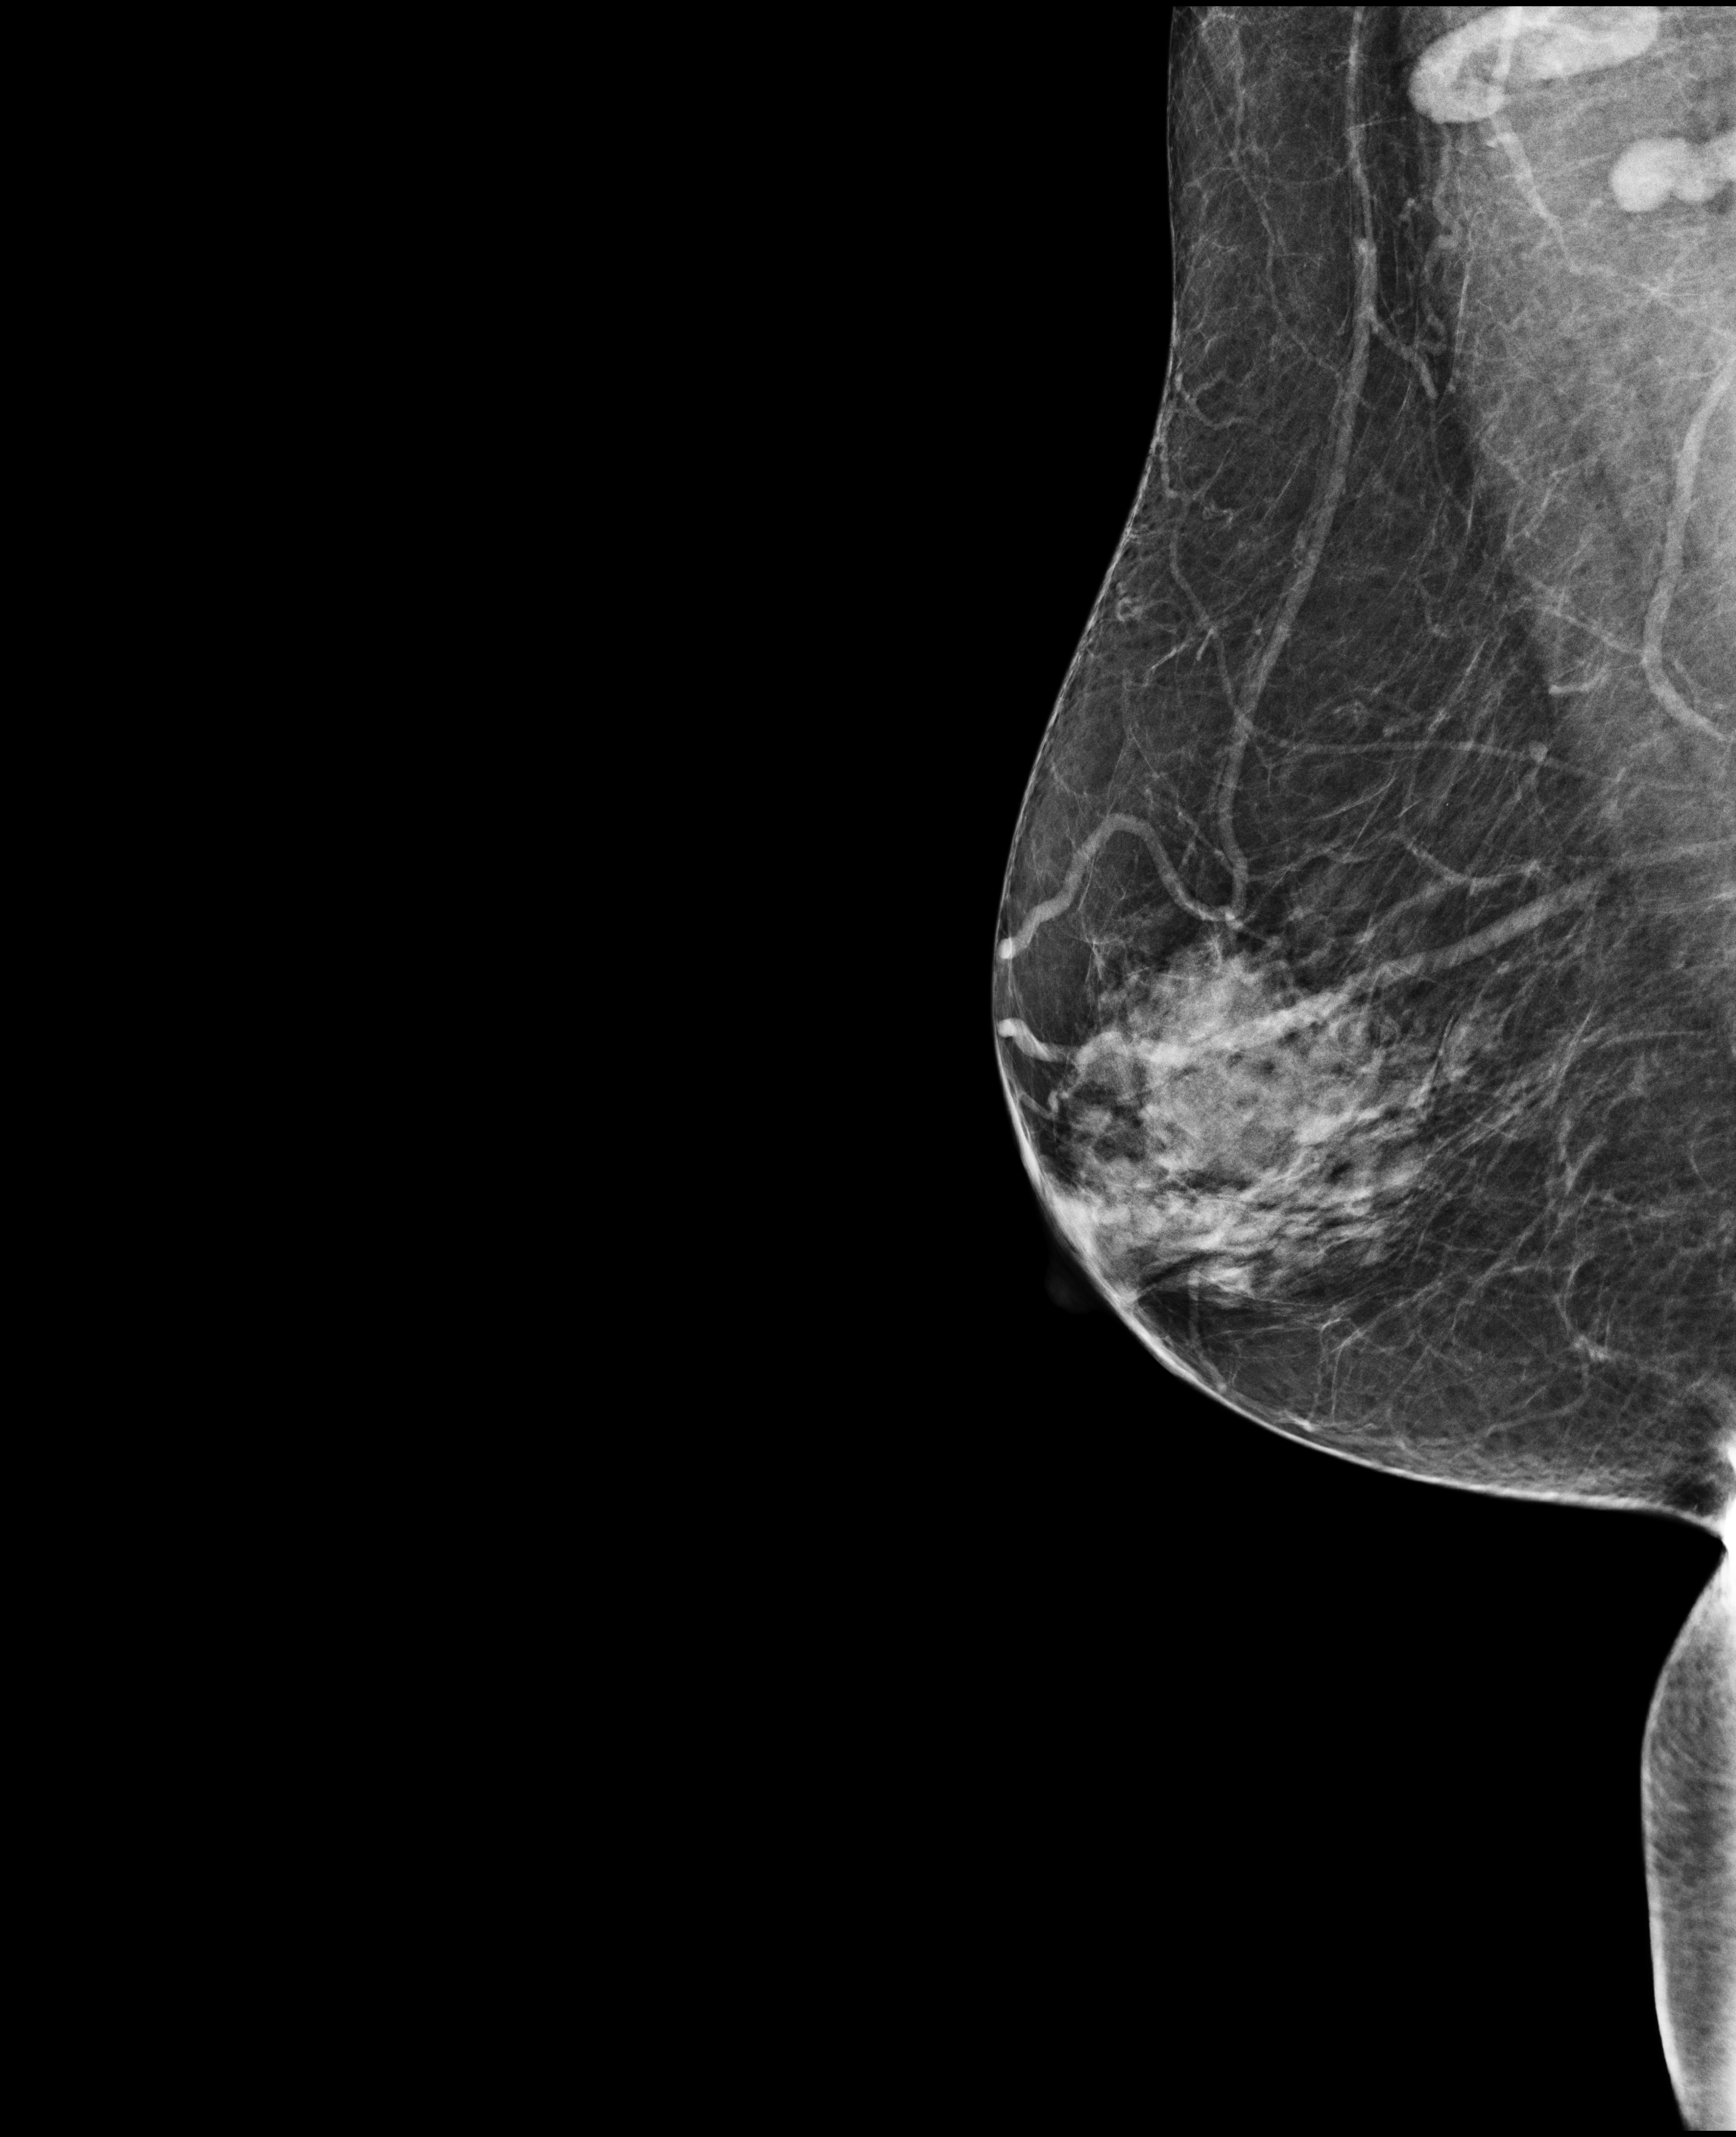
Full-field digital mammogram (FFDM), right breast, MLO view, screening examination, compressed breast thickness 46 mm, system: Selenia Dimensions. Patient aged 70 years (female).
Breast density at the screening exam (both breasts): heterogeneously dense (BI-RADS density category c). Final BI-RADS category for the screening round (tomosynthesis exam, both breasts): category 1. Recall: no recall after this screen.